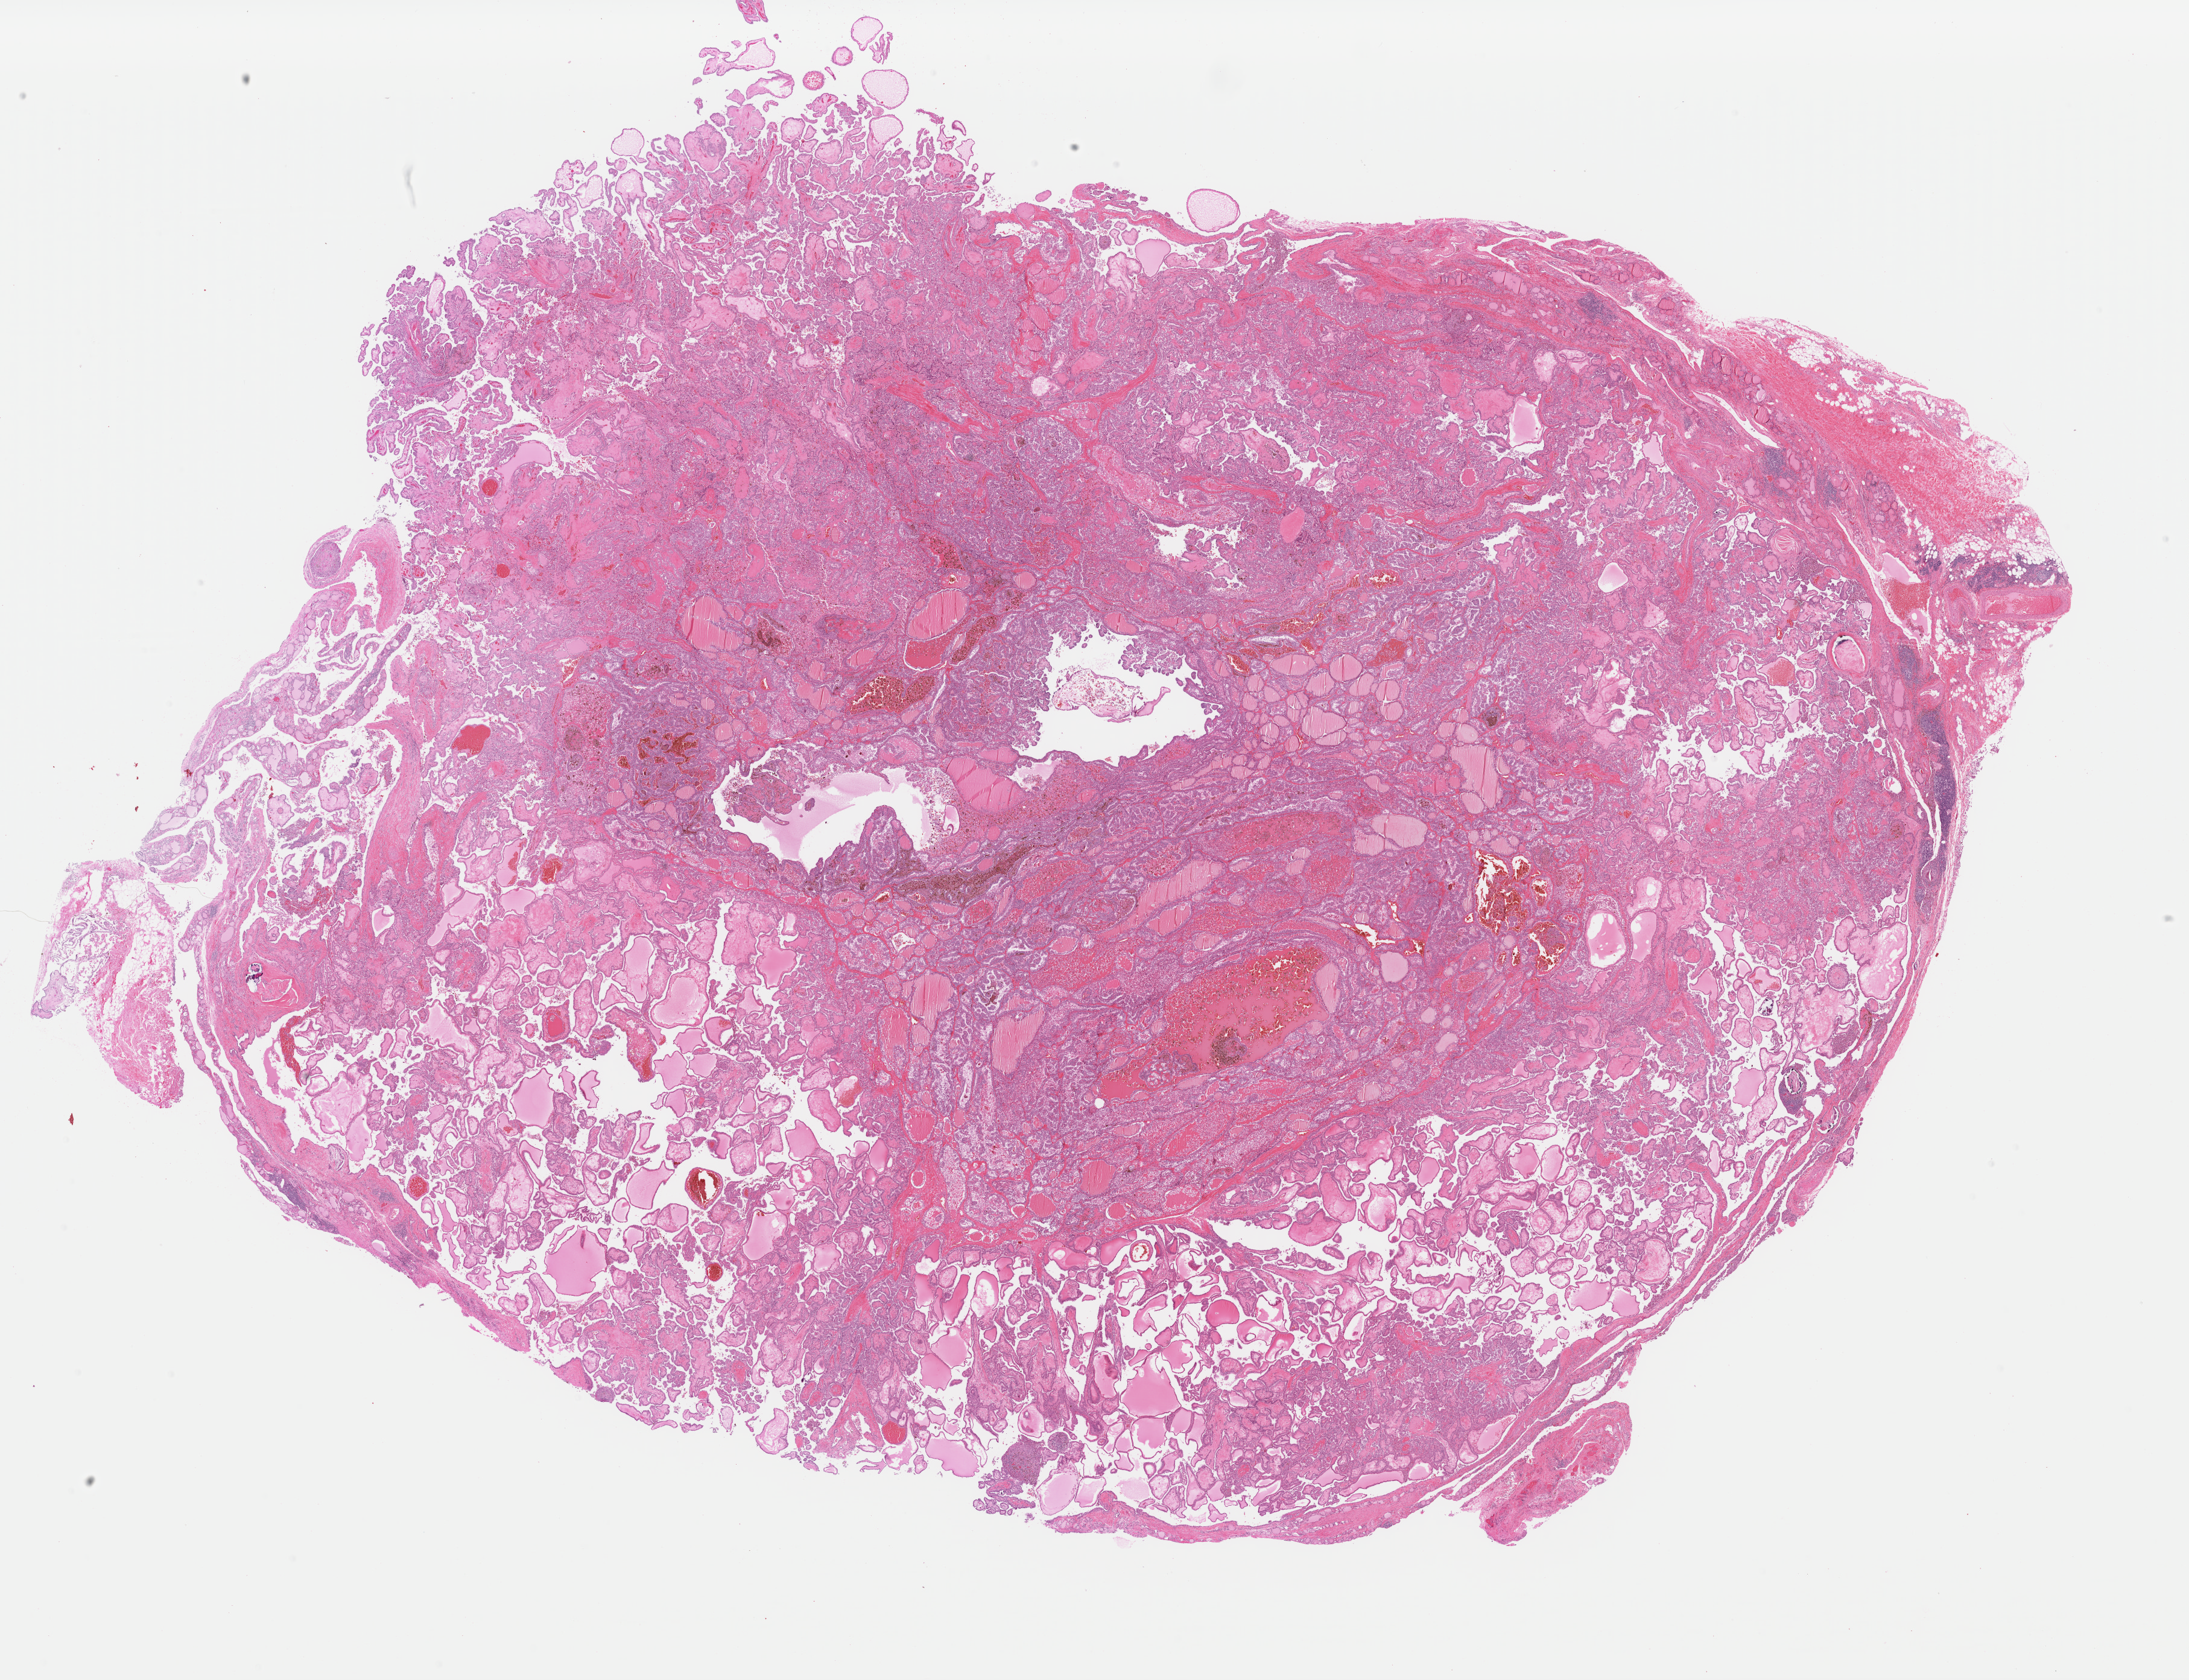
Hematoxylin and eosin (H&E) stained whole-slide image — low-resolution overview of the scanned area, about 28.7 x 22.0 mm (slide scanned at 40x), formalin-fixed paraffin-embedded (FFPE) diagnostic section, thyroid, primary tumour sample. Patient: male, age at initial diagnosis 42 years.
• AJCC pathologic stage: I
• pathologic diagnosis: Papillary adenocarcinoma, NOS (thyroid gland)